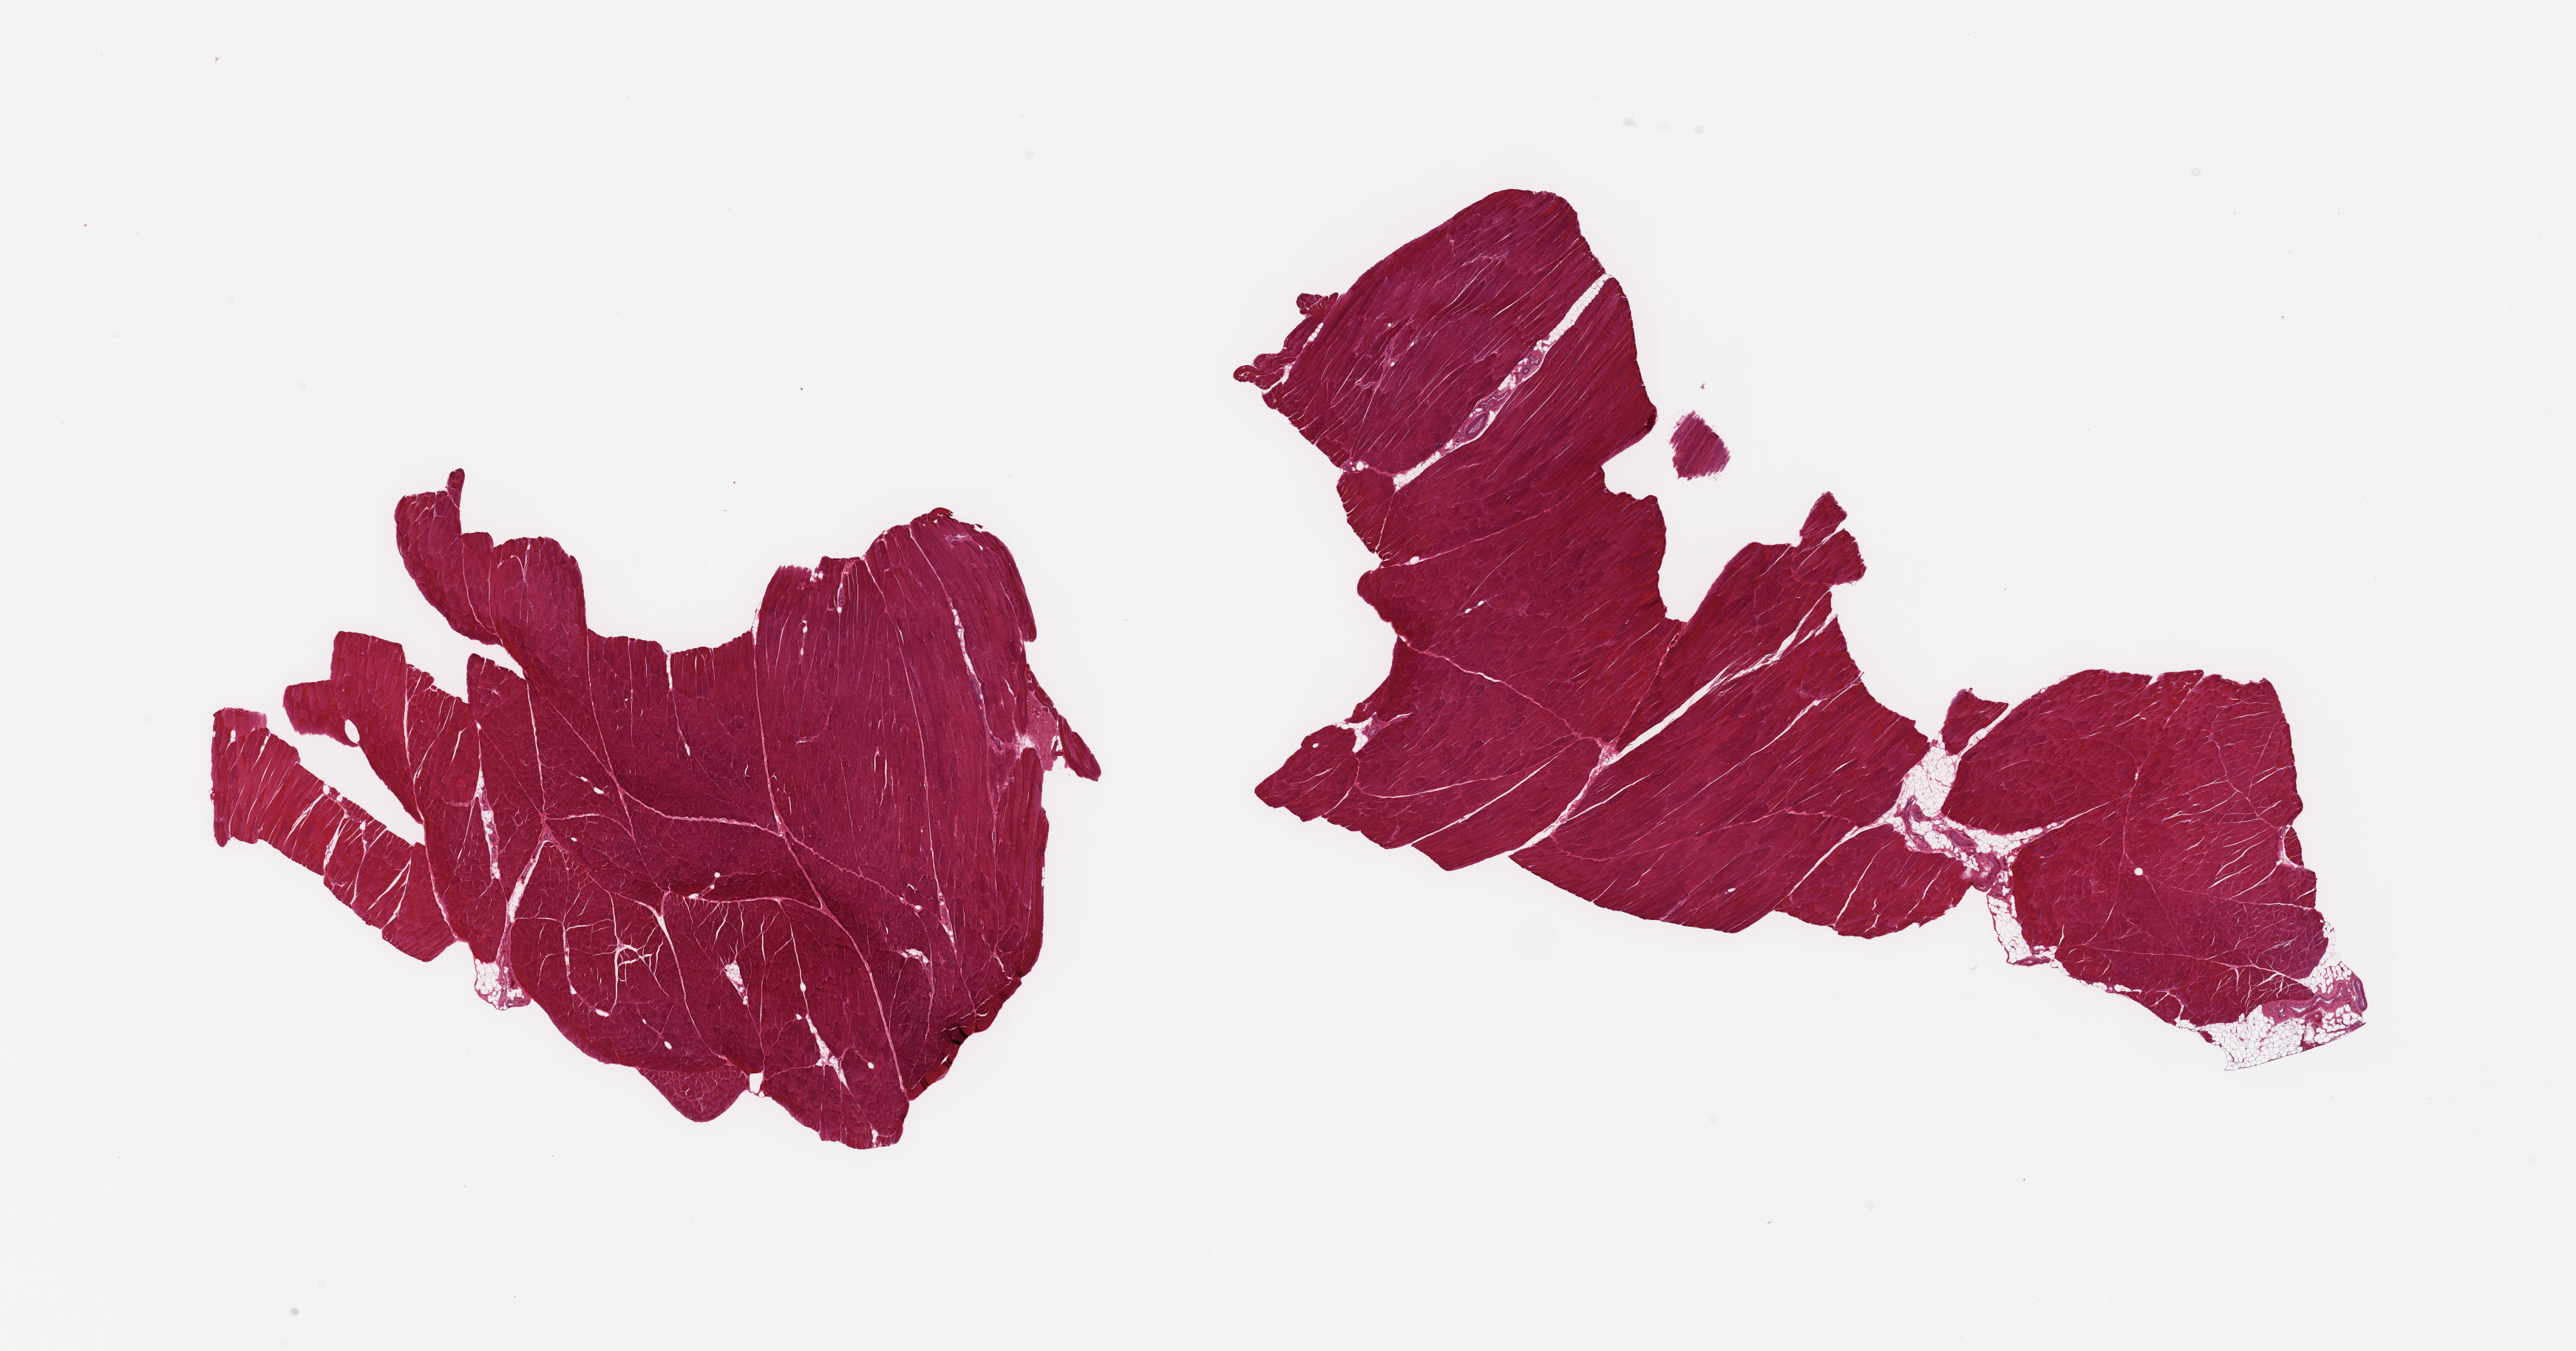
Whole-slide image, H&E stain, brightfield, low-resolution overview of the scanned area, about 27.6 x 14.5 mm, PAXgene-fixed, paraffin-embedded tissue, sampled site (target tissue): skeletal muscle, tissue donor sample.
Reviewer comment on this tissue sample: 2 pieces; one piece with trace of internal/external fat.